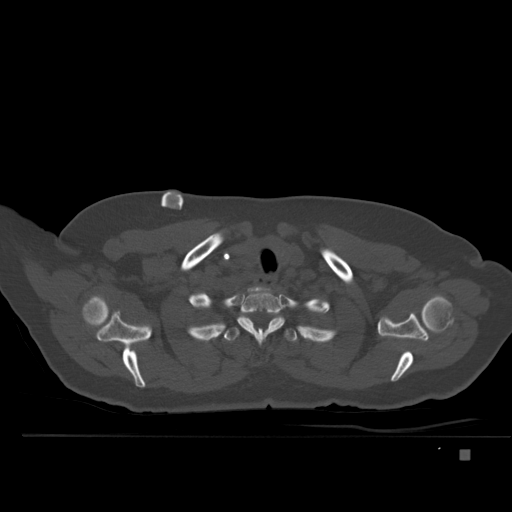
CT including the spine, one axial slice. Position 399 of 477 along the scan axis. Bone window (W 1800 / L 400 HU). 512 × 512 image matrix, field of view 422 × 422 mm. Female patient, age 74 years. From the clinical record (not read from this slice): primary cancer: colon.
Outlined on this slice (semi-automatically segmented with operator editing):
- T1 vertebra: box from (x=238, y=289) to (x=284, y=341) px
- T2 vertebra: (x=198, y=316)–(x=315, y=342)